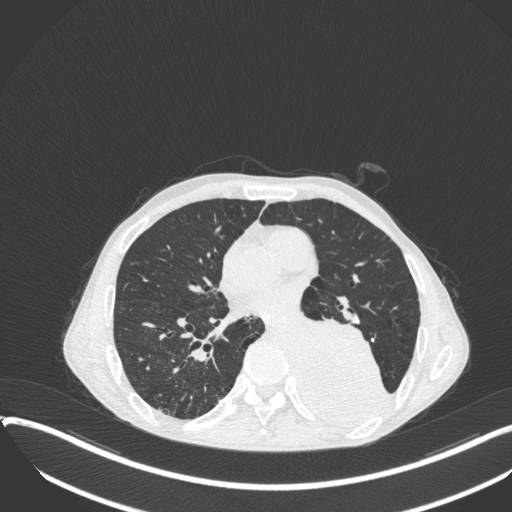
Chest CT, one axial slice; reconstruction kernel B31f; 120 kVp; lung window (W 1500 / L -600 HU); 1 mm slice thickness; 512 × 512 image matrix. Male patient, age 57 years. Case-level facts recorded for this patient, not image findings: clinical TNM (as recorded): T4 N0 M0.
Annotated regions visible in this slice (bounding box drawn by a radiologist):
- lung tumour (recorded histology: squamous cell carcinoma): bounding box [x1, y1, x2, y2] px = [296, 309, 397, 428]